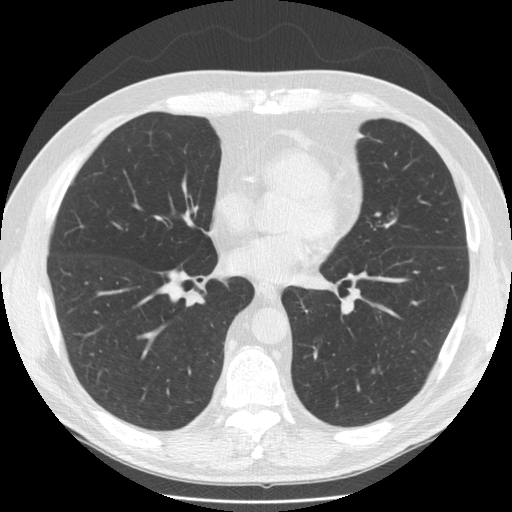
Low-dose screening chest CT, axial slice, third annual screen, lung window (W 1500 / L -600 HU), 2.5 mm slice thickness, standard (soft-tissue) reconstruction kernel (STANDARD). Male participant, aged 58 years at enrolment. Former smoker at enrolment.
Expert reader's lesion annotation, bounding box <364,357,402,382> (left, top, right, bottom; pixels). Screening reader's record for this exam (one nodule recorded; not confirmed to be the boxed lesion): non-calcified nodule or mass ≥4 mm, left lower lobe, 10 × 7 mm, smooth margins, soft tissue attenuation, pre-existing on the prior screen: yes; interval growth: yes. Official screen result: positive, other. Lung cancer was diagnosed 49 days after this screen: adenocarcinoma, NOS, left lower lobe, poorly differentiated (G3), stage IA (AJCC 6th edition), 8 mm at pathology.